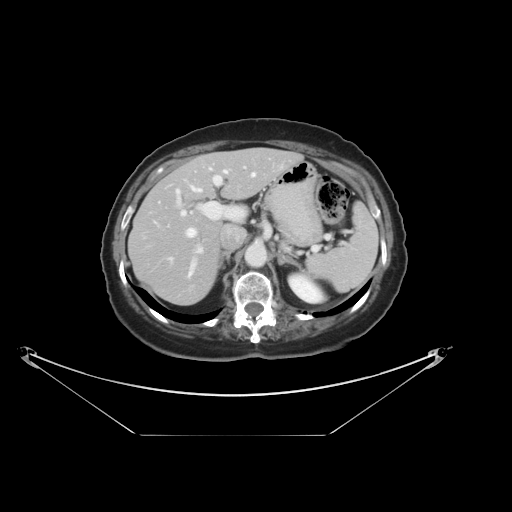
Contrast-enhanced abdominal CT, one axial slice; position 23 of 36 along the scan axis; reconstruction kernel STANDARD; 120 kVp; intravenous contrast given; soft-tissue window (W 400 / L 40 HU); 512 × 512 image matrix, field of view 500 × 500 mm. Female patient, age 70 years. From the clinical record (not read from this slice): diagnosis: colorectal cancer liver metastases, imaged before liver resection; multiple liver metastases: no; largest metastasis: 2.5 cm.
Structures marked on this image (manually delineated by an expert):
- hepatic veins: bounding box (x1, y1, x2, y2) in pixels: (141, 168, 255, 239)
- liver: (130, 149, 301, 306)
- planned liver remnant (the part of the liver to remain after resection): (130, 149, 301, 306)
- portal vein (with intrahepatic branches): (168, 167, 245, 279)